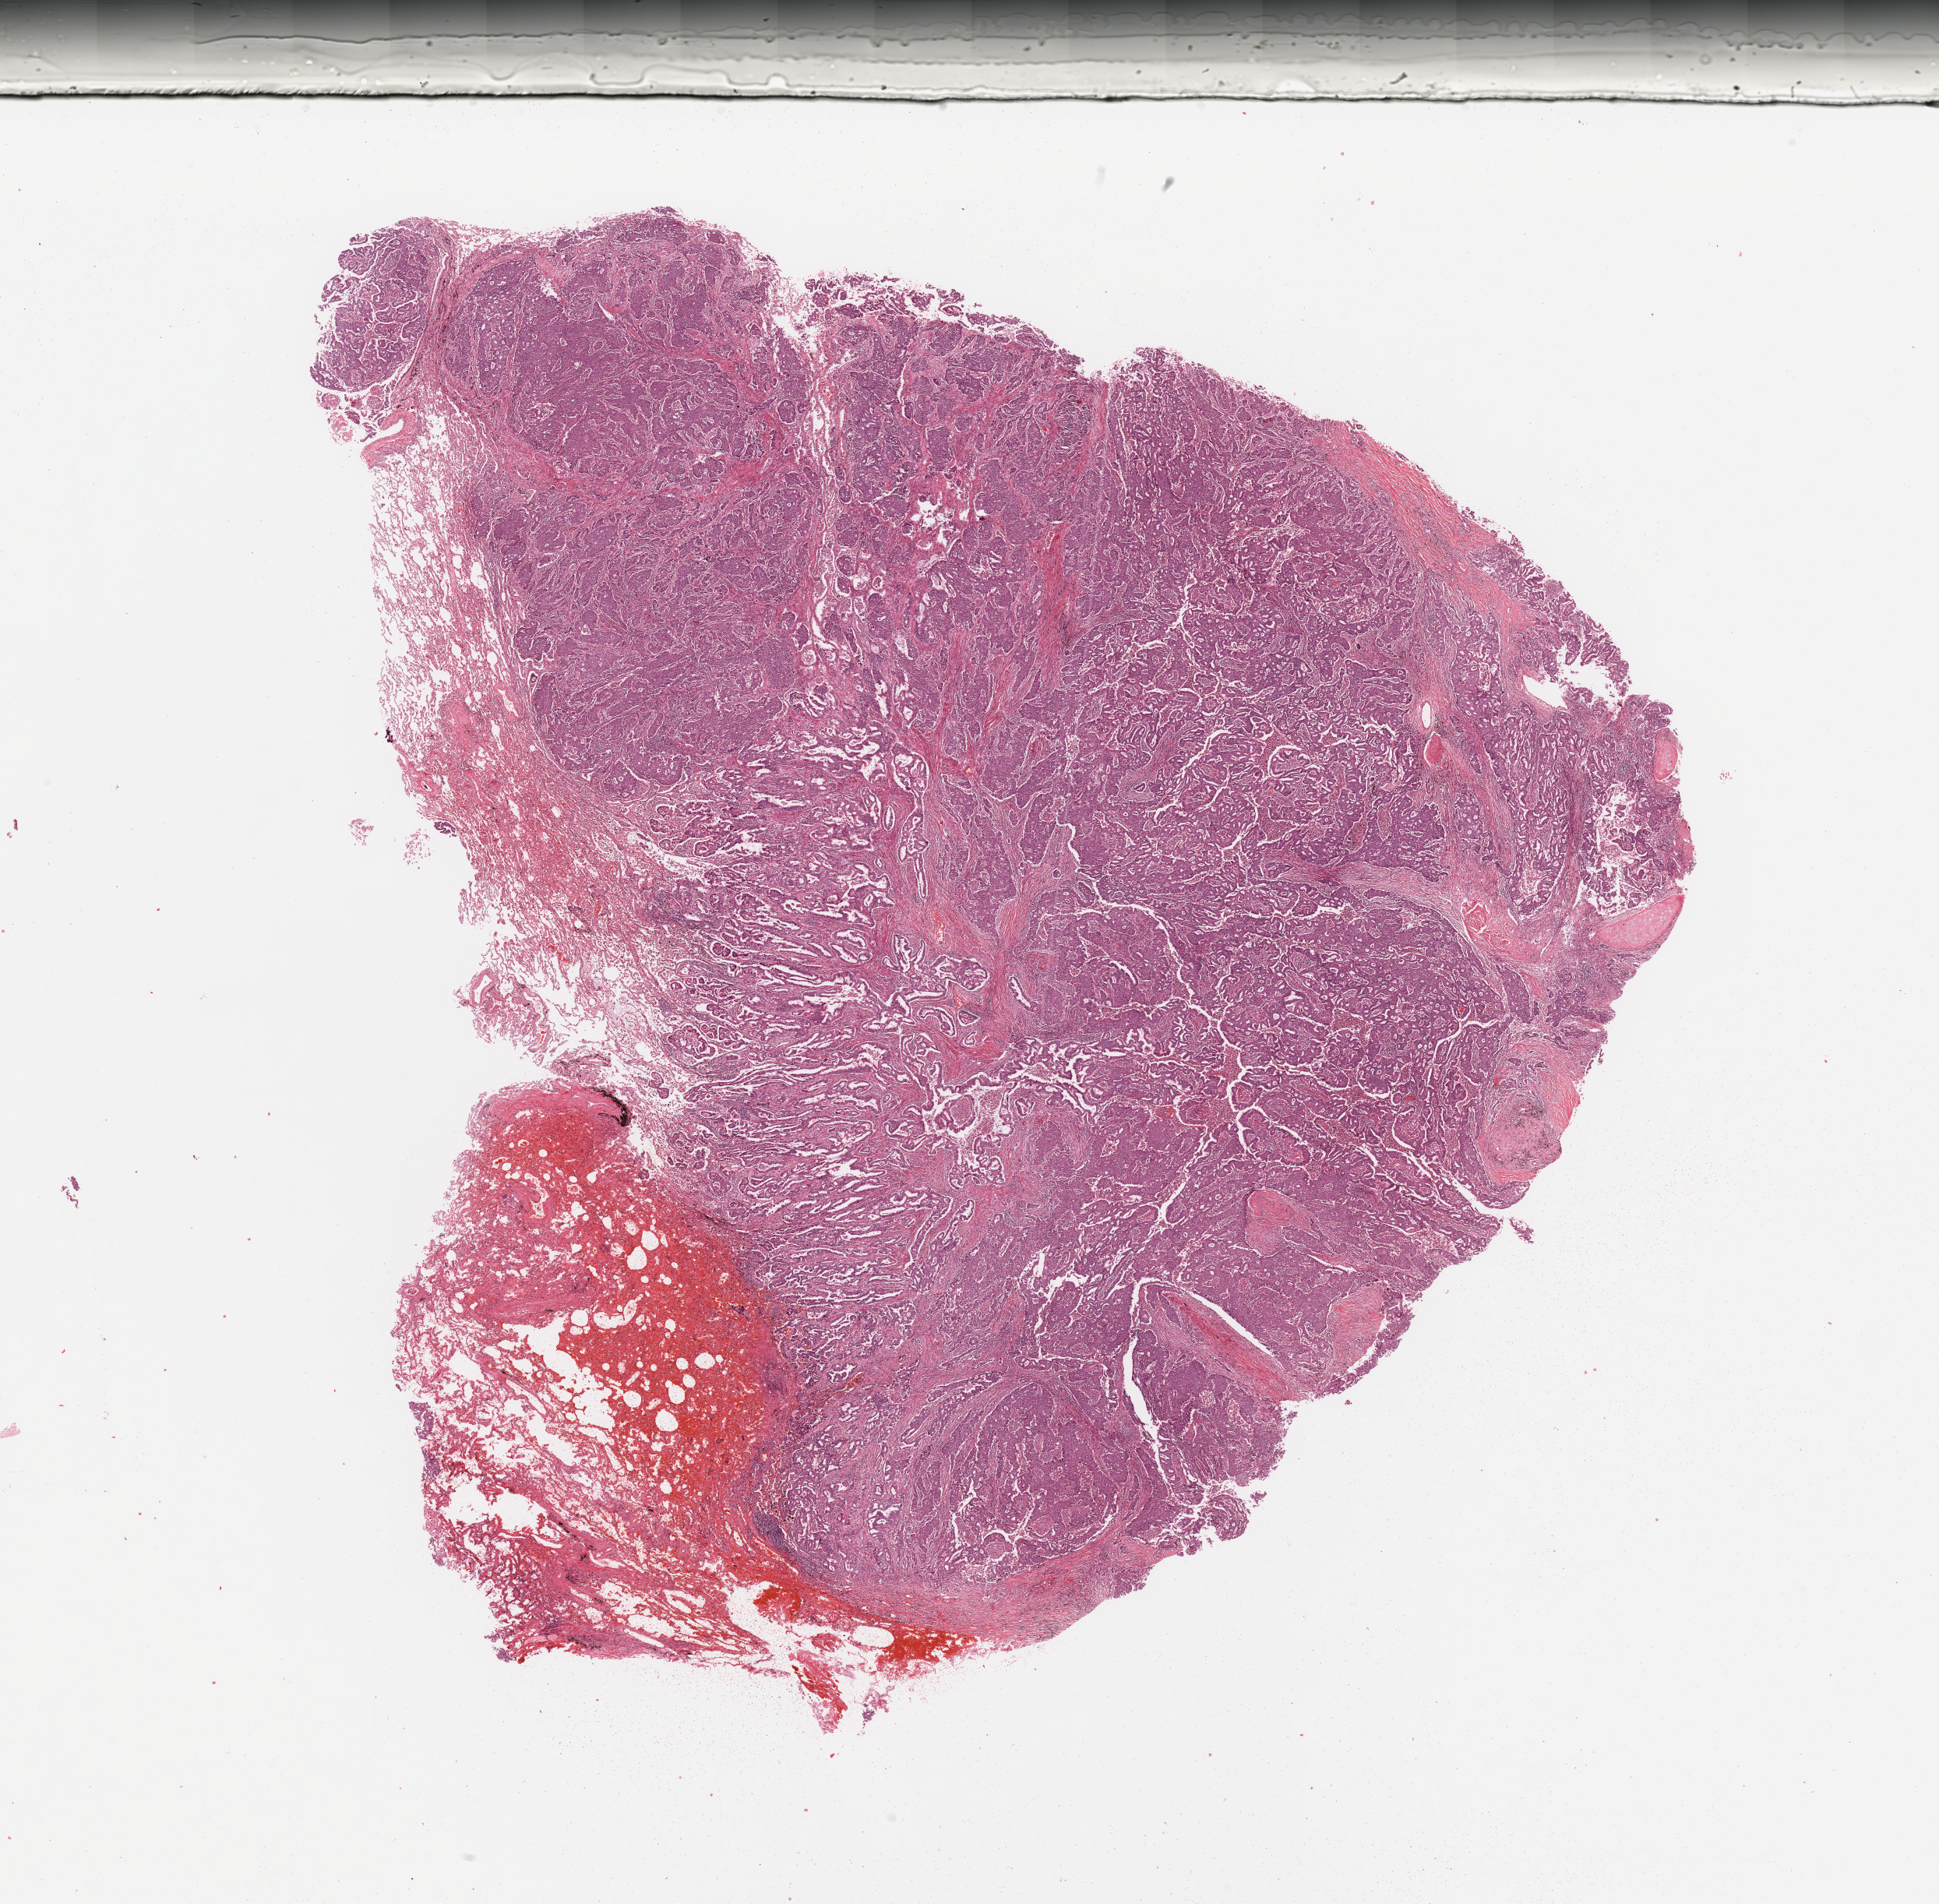
Whole-slide histology image, Hematoxylin and eosin (H&E) stained — a low-resolution overview of the entire scanned area, about 19.7 x 19.3 mm (from a 20x scan); tumour tissue sample, lung. Male, 67 y/o. Histologic grade: G2 (moderately differentiated).
- AJCC pathologic stage: IB
- diagnosis: Adenocarcinoma, NOS